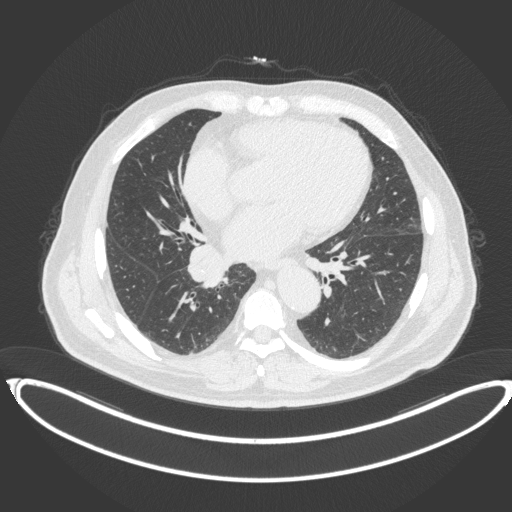
Chest CT, one axial slice; slice 184 of 383 in the series (ordered by position); 120 kVp; lung window (W 1500 / L -600 HU); 512 × 512 image matrix, field of view 448 × 448 mm. Patient: male, 61 years. From the clinical record (not read from this slice): clinical TNM (as recorded): T1b N1 M0.
Structures marked on this image (rectangle marked by the reading radiologist):
- lung tumour (recorded histology: squamous cell carcinoma): box from (x=188, y=240) to (x=227, y=292) px